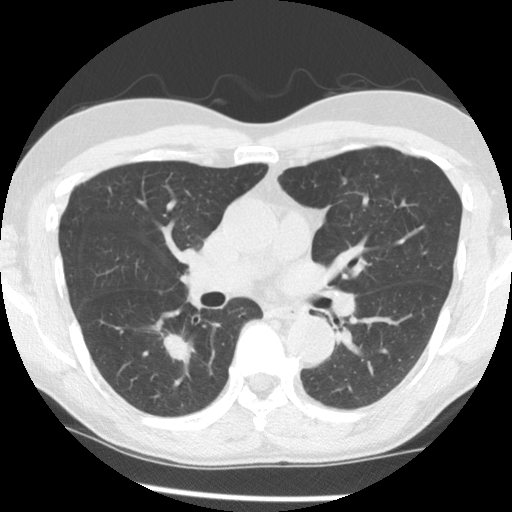
Axial slice from a low-dose chest CT screening exam, third annual screen, lung window (W 1500 / L -600 HU), standard (soft-tissue) reconstruction kernel (STANDARD), 140 kVp, 512 × 512 image matrix, field of view 320 × 320 mm. Male, age 65 years at enrolment.
• Lesion marked by an expert reader, bounding box <147,322,207,377> (left, top, right, bottom; pixels).
• The screening reader recorded 2 non-calcified nodules or masses ≥4 mm on this exam; which of them this box marks is not recorded.
• Lung cancer was diagnosed 116 days after this screen: adenocarcinoma, NOS, right lower lobe, poorly differentiated (G3), stage IA (AJCC 6th edition), 18 mm at pathology.